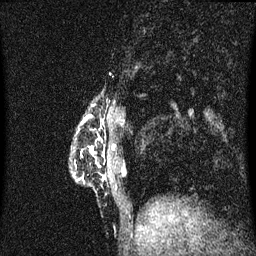
Breast MRI (dynamic contrast-enhanced), one sagittal slice; slice 11 of 60 in the series (ordered by position); dynamic contrast-enhanced series, image 2 of 3 at this slice position (ordered by acquisition); 1.5 T; TE 4.2 ms, TR 8.4 ms; 256 × 256 image matrix, field of view 200 × 200 mm. Female patient, age 40 years.
Structures marked on this image (semi-automatically segmented with operator editing):
- analysis volume of interest (the breast-tissue region the enhancement analysis was run in; not a lesion): bounding box [x1, y1, x2, y2] px = [73, 114, 107, 179]
- tumour enhancement mask (voxels above the 70 % enhancement threshold inside the analysis volume of interest): [82, 122, 94, 155]